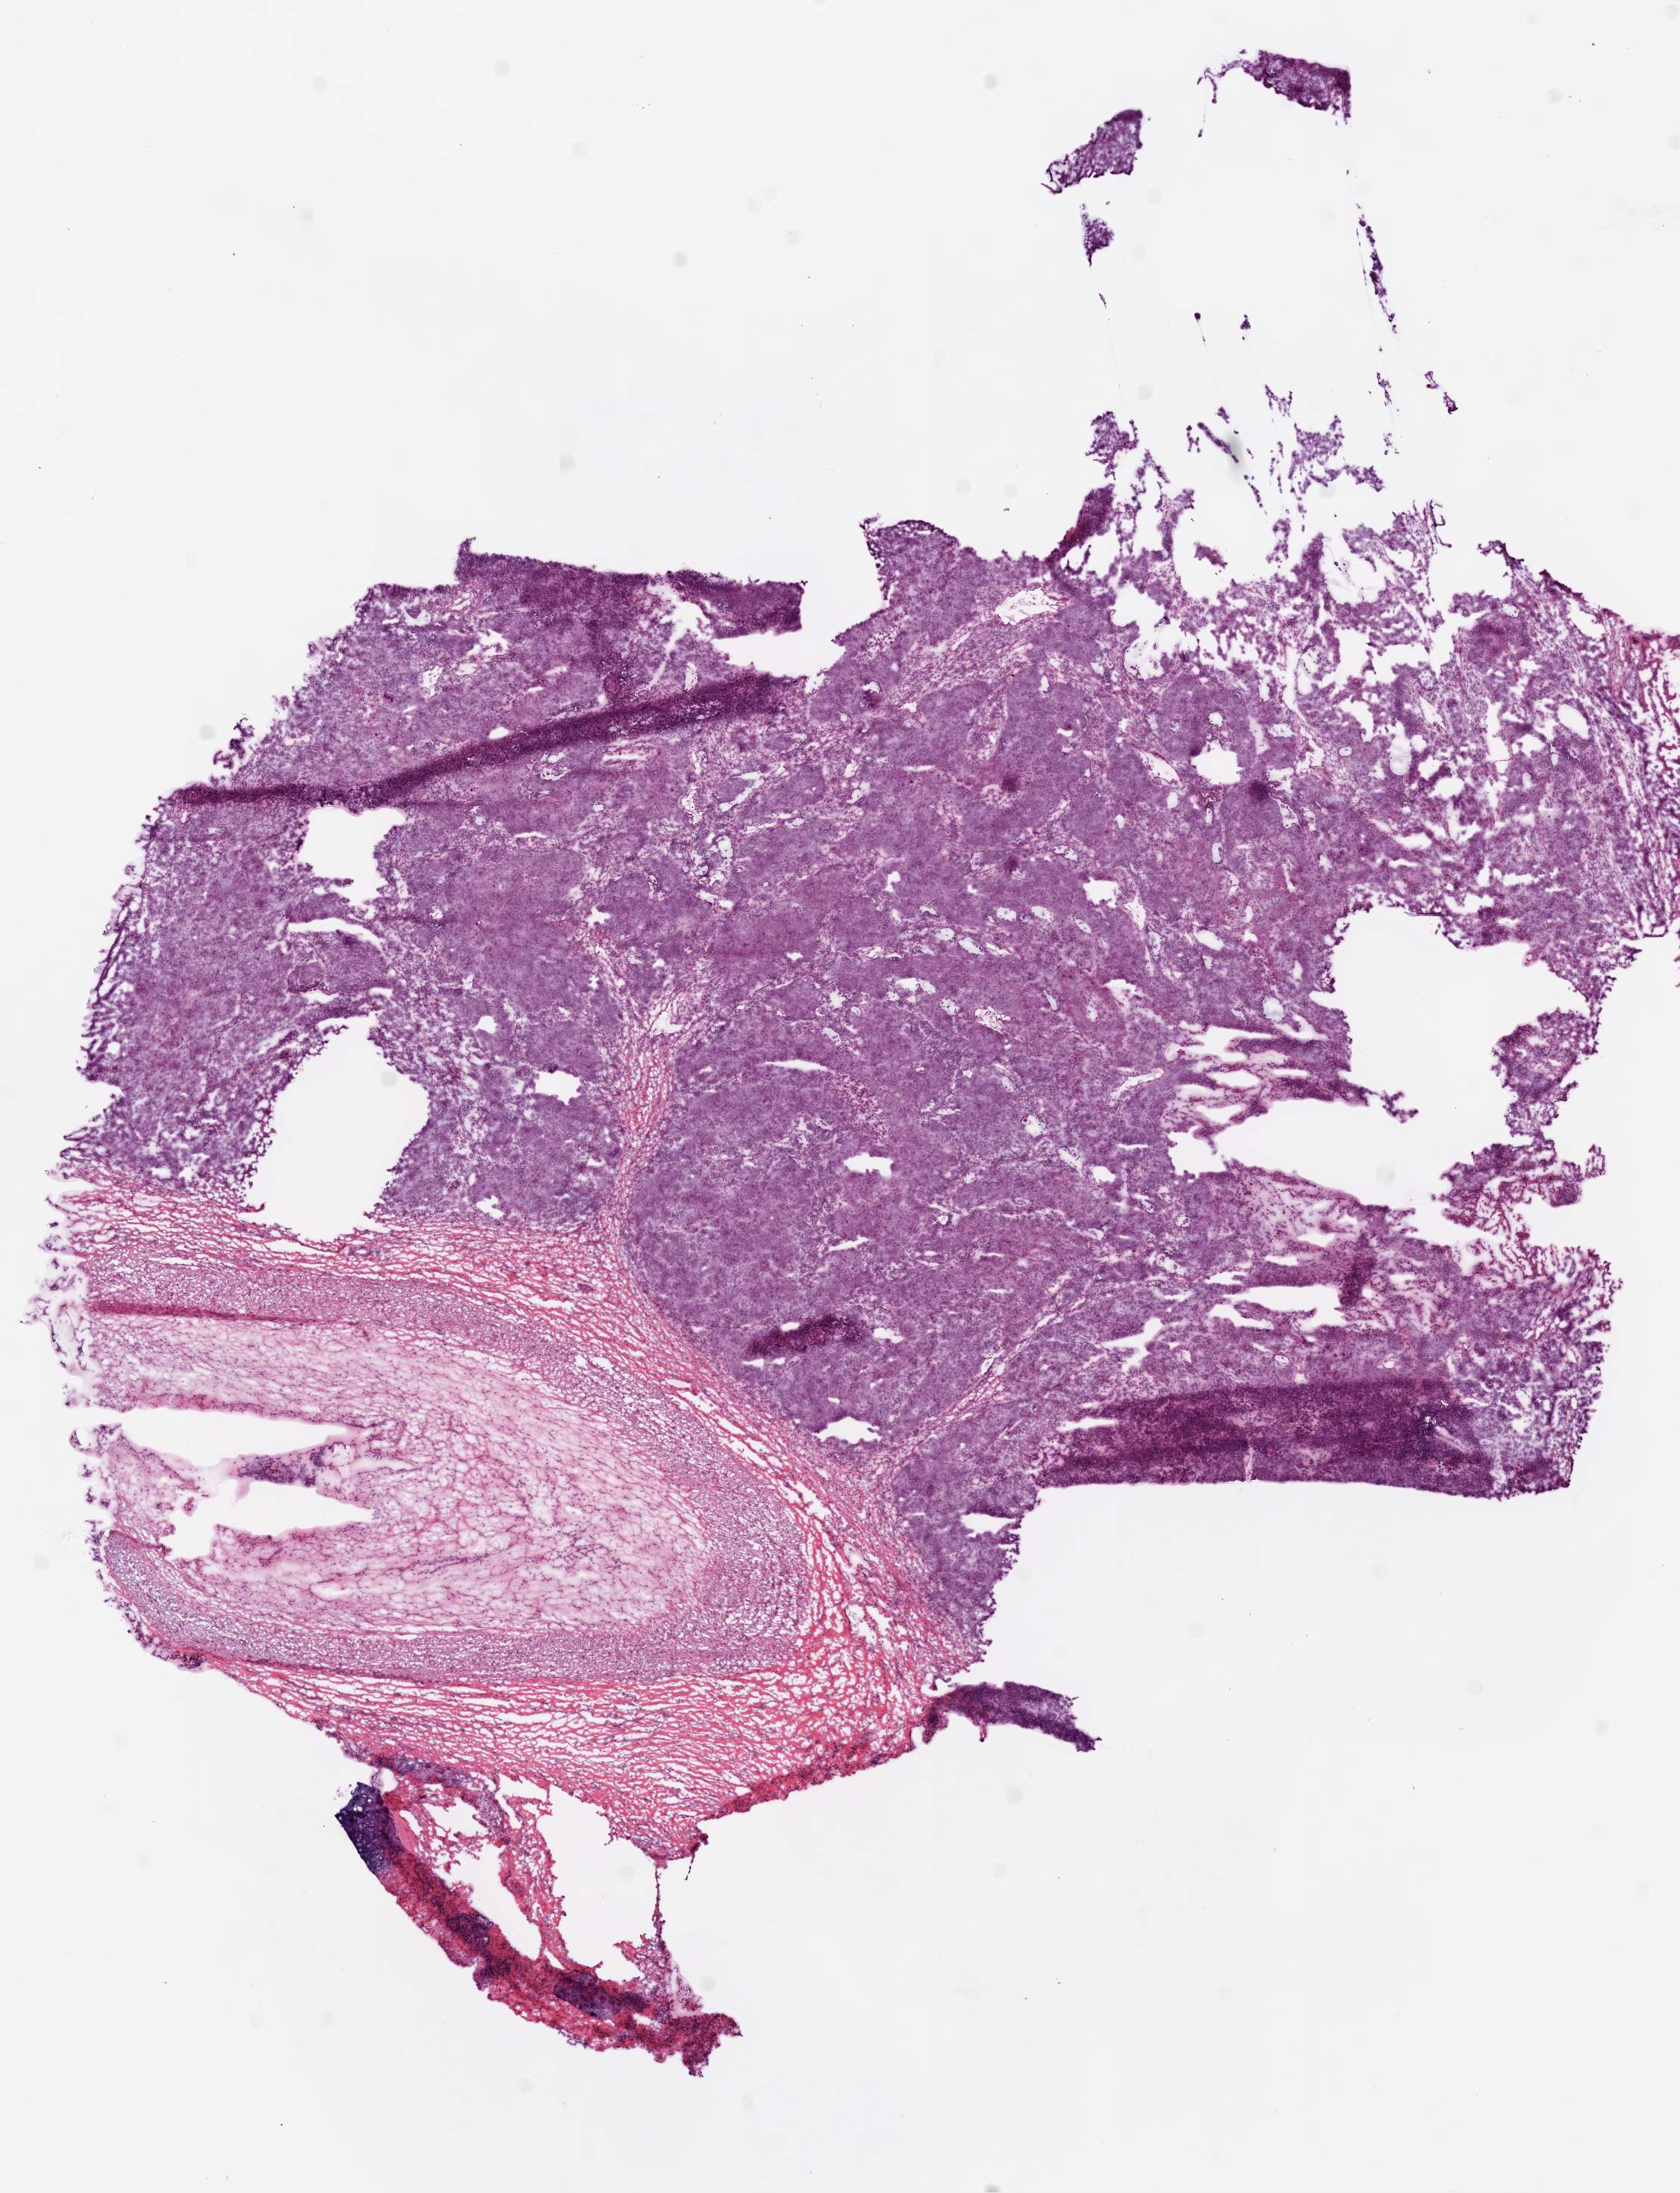
Digitized Hematoxylin and eosin (H&E) stained tissue section (whole slide), whole scanned area (about 9.0 x 11.8 mm) shown as a low-resolution overview; frozen section from the top of the tissue portion; sample: primary tumour, lung. Male patient; age at initial diagnosis 65 years. Pathologist review of this section (percent, as recorded): tumour cells 65%, tumour nuclei 80%, normal cells 25%, stromal cells 5%, necrosis 5%.
AJCC pathologic stage: IB. Pathologic diagnosis: Squamous cell carcinoma, NOS (lower lobe, lung). Laterality: right.